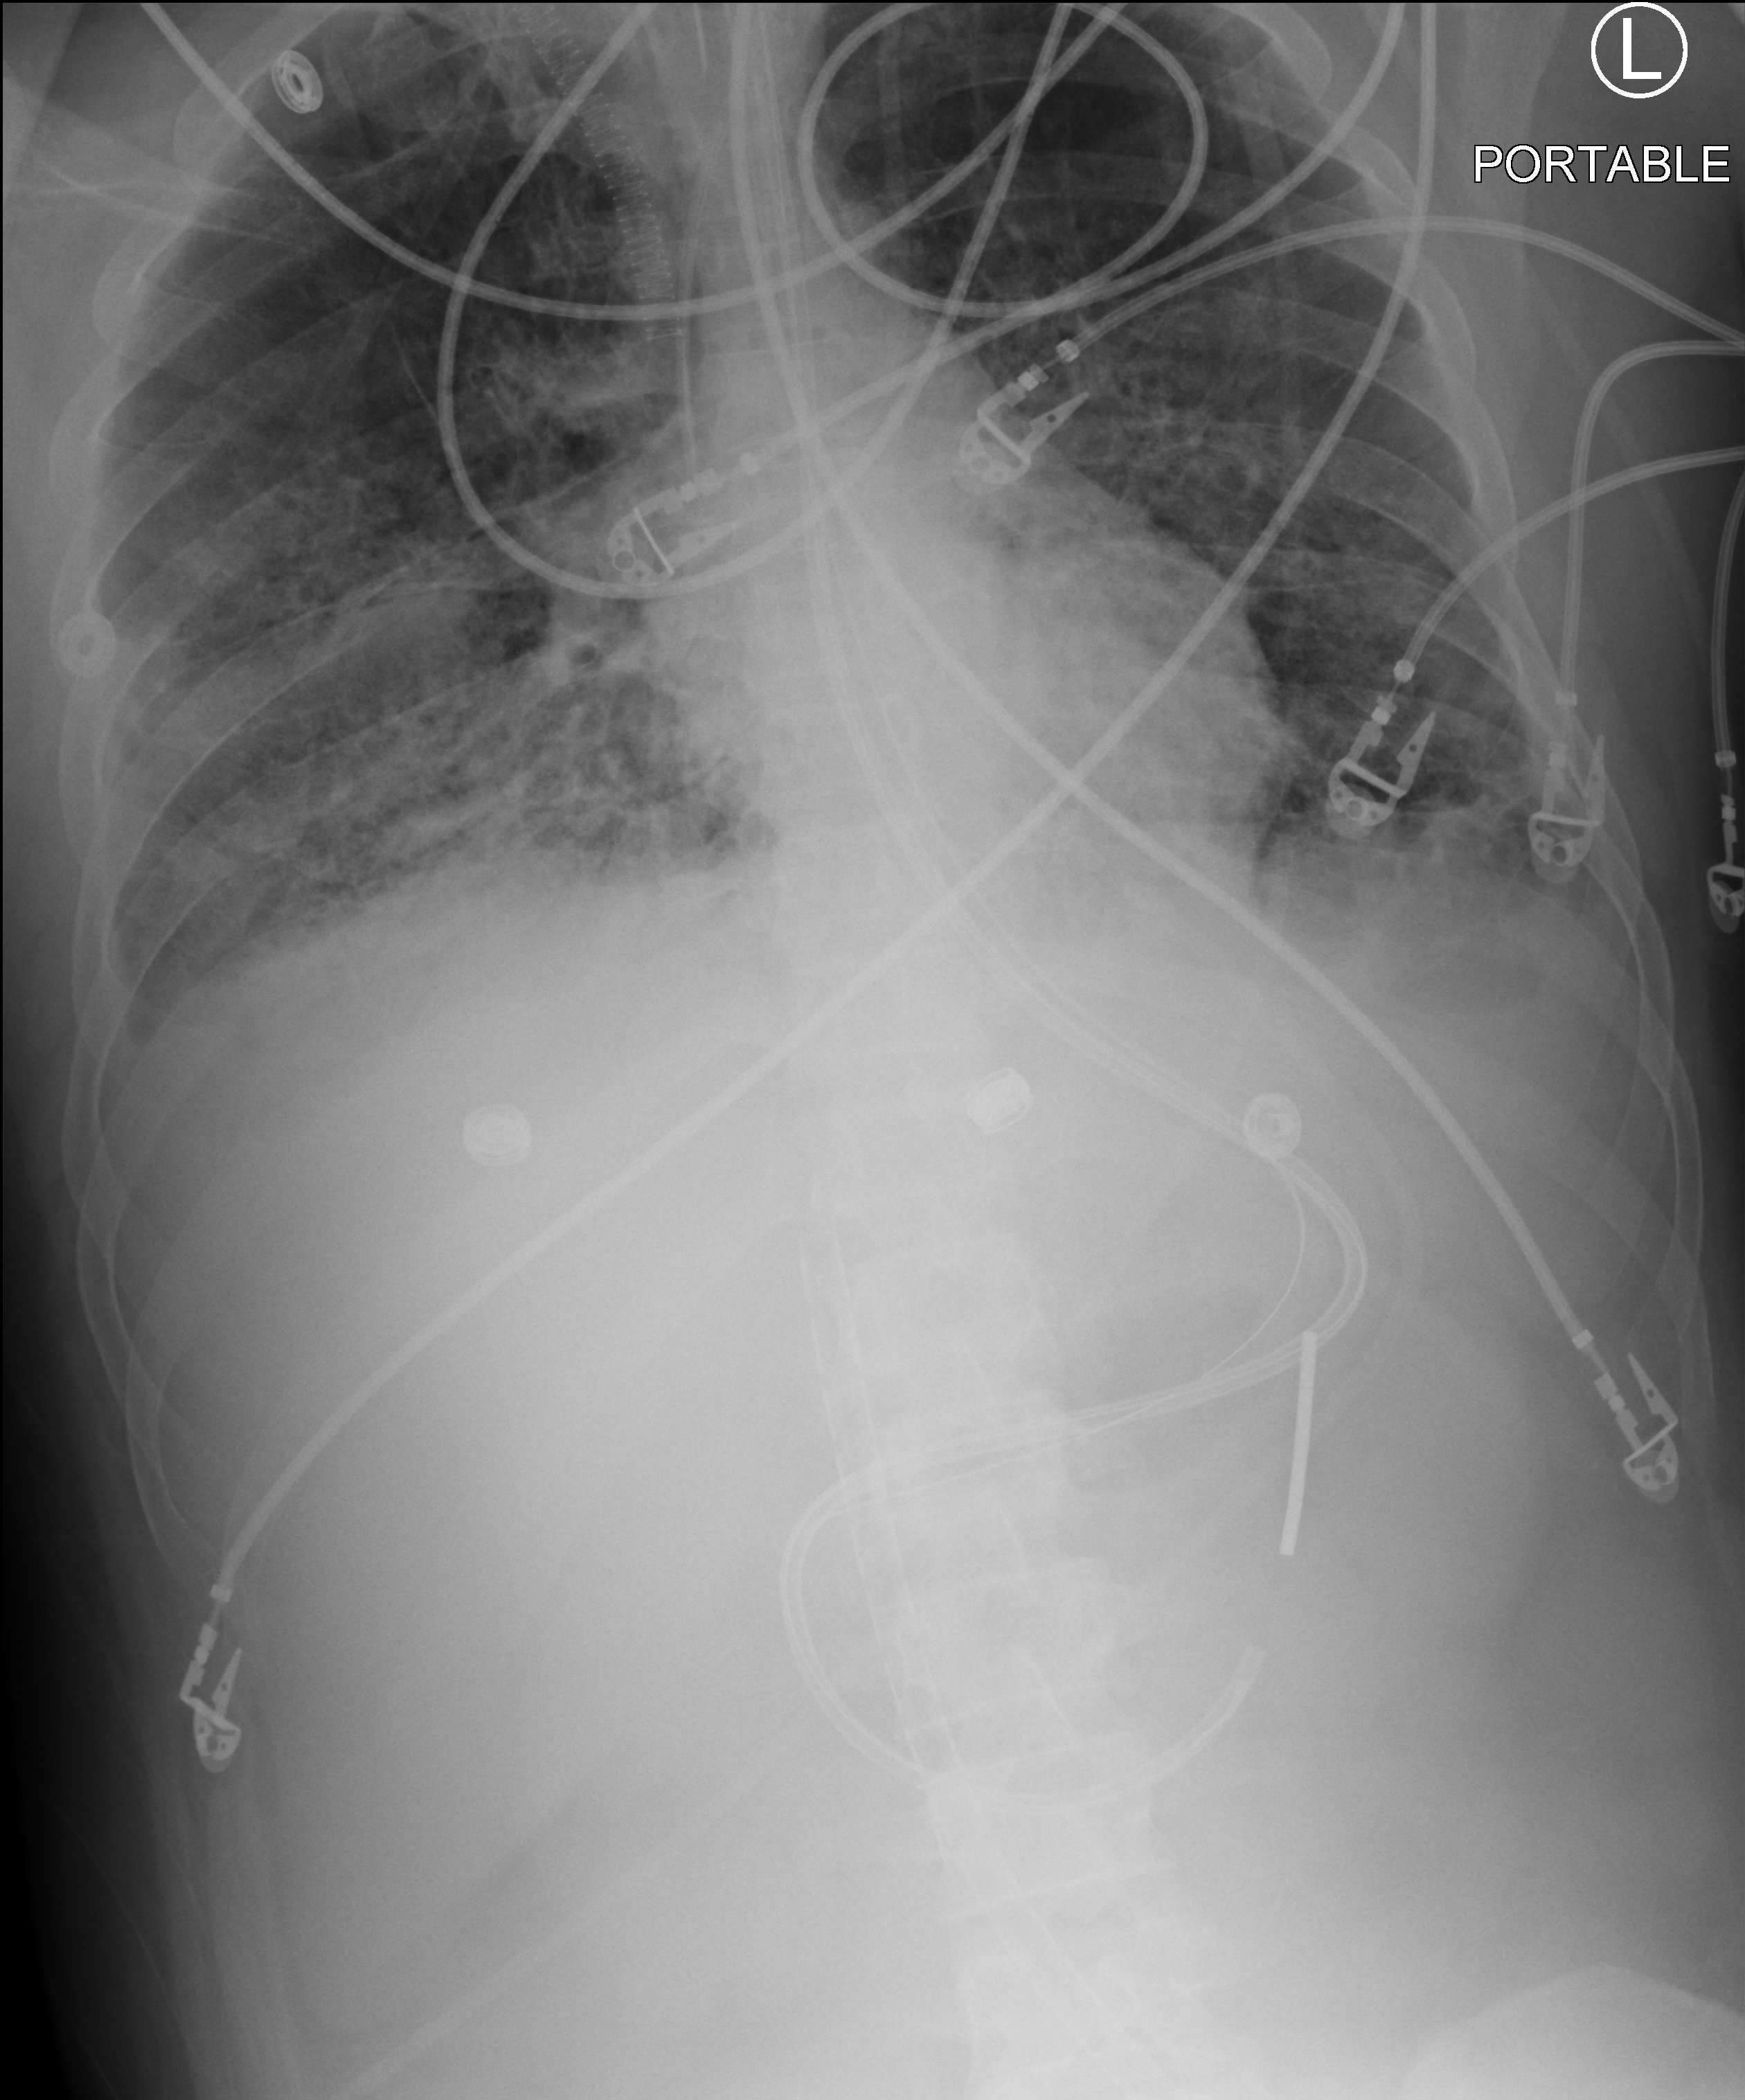
Chest X-ray (portable). Adult patient hospitalised with COVID-19, age 18–59 years.
Admission-level facts for this patient (not findings on this image; timing relative to this image not recorded):
- mechanically ventilated during this hospital stay: yes
- admitted to intensive care during this hospital stay: yes